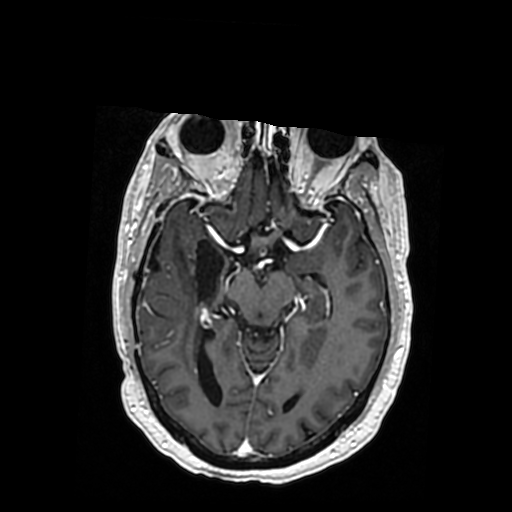
Brain MRI from a brain-tumour surgery series, one axial slice. Slice 208 of 364 in the series (ordered by position). T1-weighted post-contrast. 512 × 512 image matrix, field of view 260 × 260 mm. Case-level facts recorded for this patient, not image findings: histopathology: Oligodendroglioma; WHO grade: 3; IDH mutation: yes.
Outlined on this slice (manually delineated by an expert):
- previous resection cavity: bounding box (x1, y1, x2, y2) in pixels: (149, 239, 236, 300)